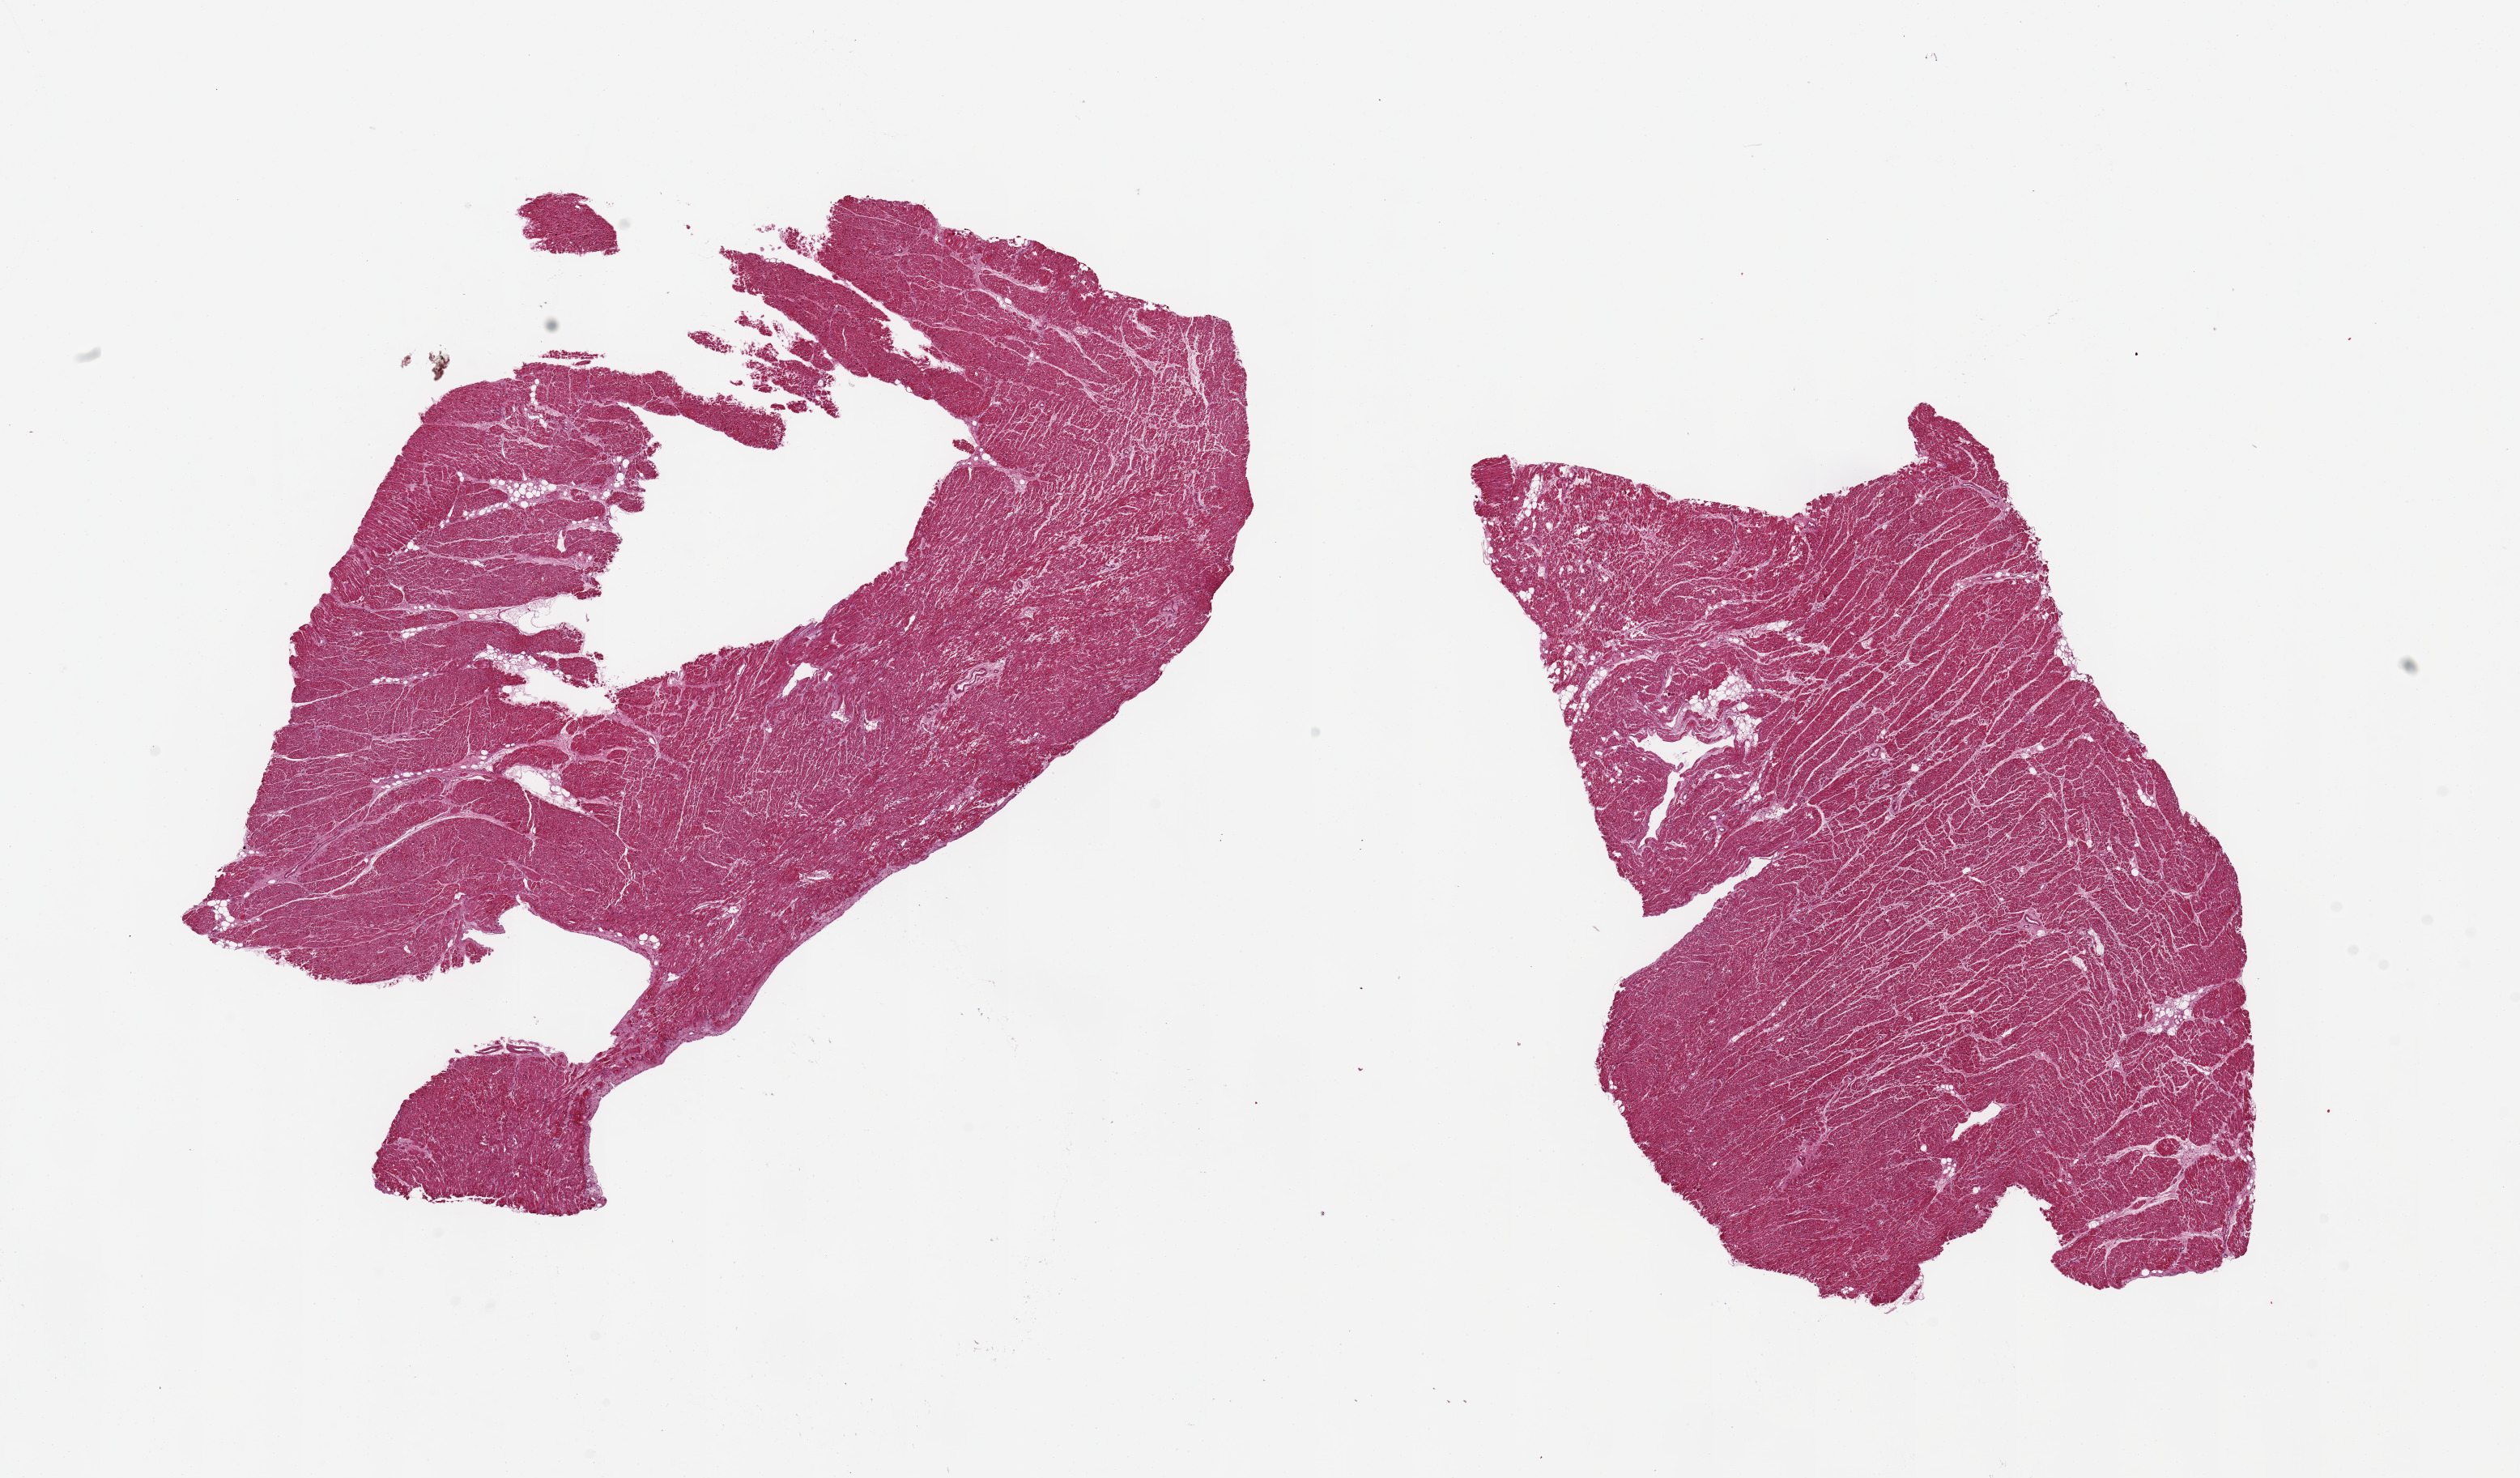
Hematoxylin and eosin (H&E) whole-slide image, shown as a low-resolution overview of the whole scanned area (about 24.6 x 14.4 mm). PAXgene-fixed paraffin-embedded (PFPE) section. Section of heart (target tissue). Donor tissue sample.
- pathologist's review note for this sample: 2 pieces, 12x8 & 11x6mm; mild interstitial fibrossi